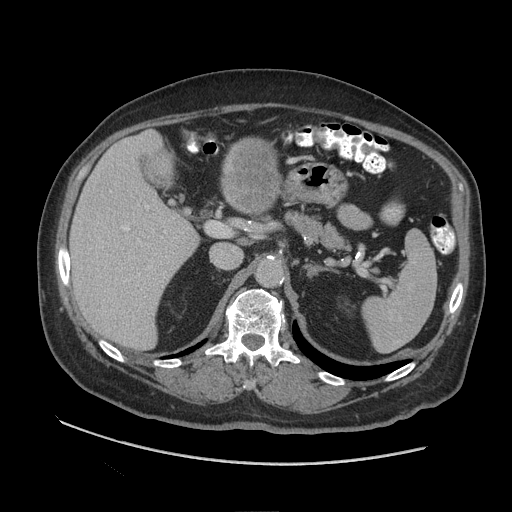
Contrast-enhanced abdominal CT (liver protocol), one axial slice; position 53 of 109 along the scan axis; reconstruction kernel STANDARD; 140 kVp; soft-tissue window (W 400 / L 40 HU); 512 × 512 image matrix, field of view 420 × 420 mm. Case-level facts recorded for this patient, not image findings: diagnosis: hepatocellular carcinoma (patient treated with transarterial chemoembolisation; whether this scan precedes or follows treatment is not stated here); TNM stage (as recorded): Stage-I.
Structures marked on this image (semi-automatic segmentation, software-assisted and operator-edited):
- liver parenchyma outside the tumour (the mass and vessels are separate outlines, so this box may not span the whole liver): bounding box <70,130,198,350> (left, top, right, bottom; pixels)
- mass: <222,137,282,212>
- liver vessels: <121,206,166,275>